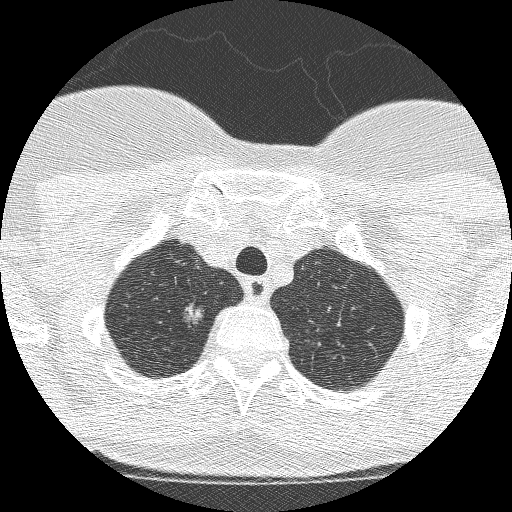
Axial slice from a low-dose chest CT screening exam; second annual screen; lung window (W 1500 / L -600 HU); slice 213 of 250 in the series; 512 × 512 image matrix. Female, age 61 years at enrolment.
Lesion marked by an expert reader, box from (x=169, y=297) to (x=215, y=335) px. Screening reader's record for this exam (one nodule recorded; not confirmed to be the boxed lesion): non-calcified nodule or mass ≥4 mm, right upper lobe, 11 × 8 mm, poorly defined margins, mixed attenuation, pre-existing on the prior screen: yes; interval growth: yes. Official screen result: positive, change unspecified: nodule(s) >= 4 mm or enlarging nodule(s), mass(es), or other non-specific abnormalities suspicious for lung cancer. Participant outcome: lung cancer diagnosed 28 days after this screen — adenocarcinoma, NOS, right upper lobe, poorly differentiated (G3), 12 mm at pathology.